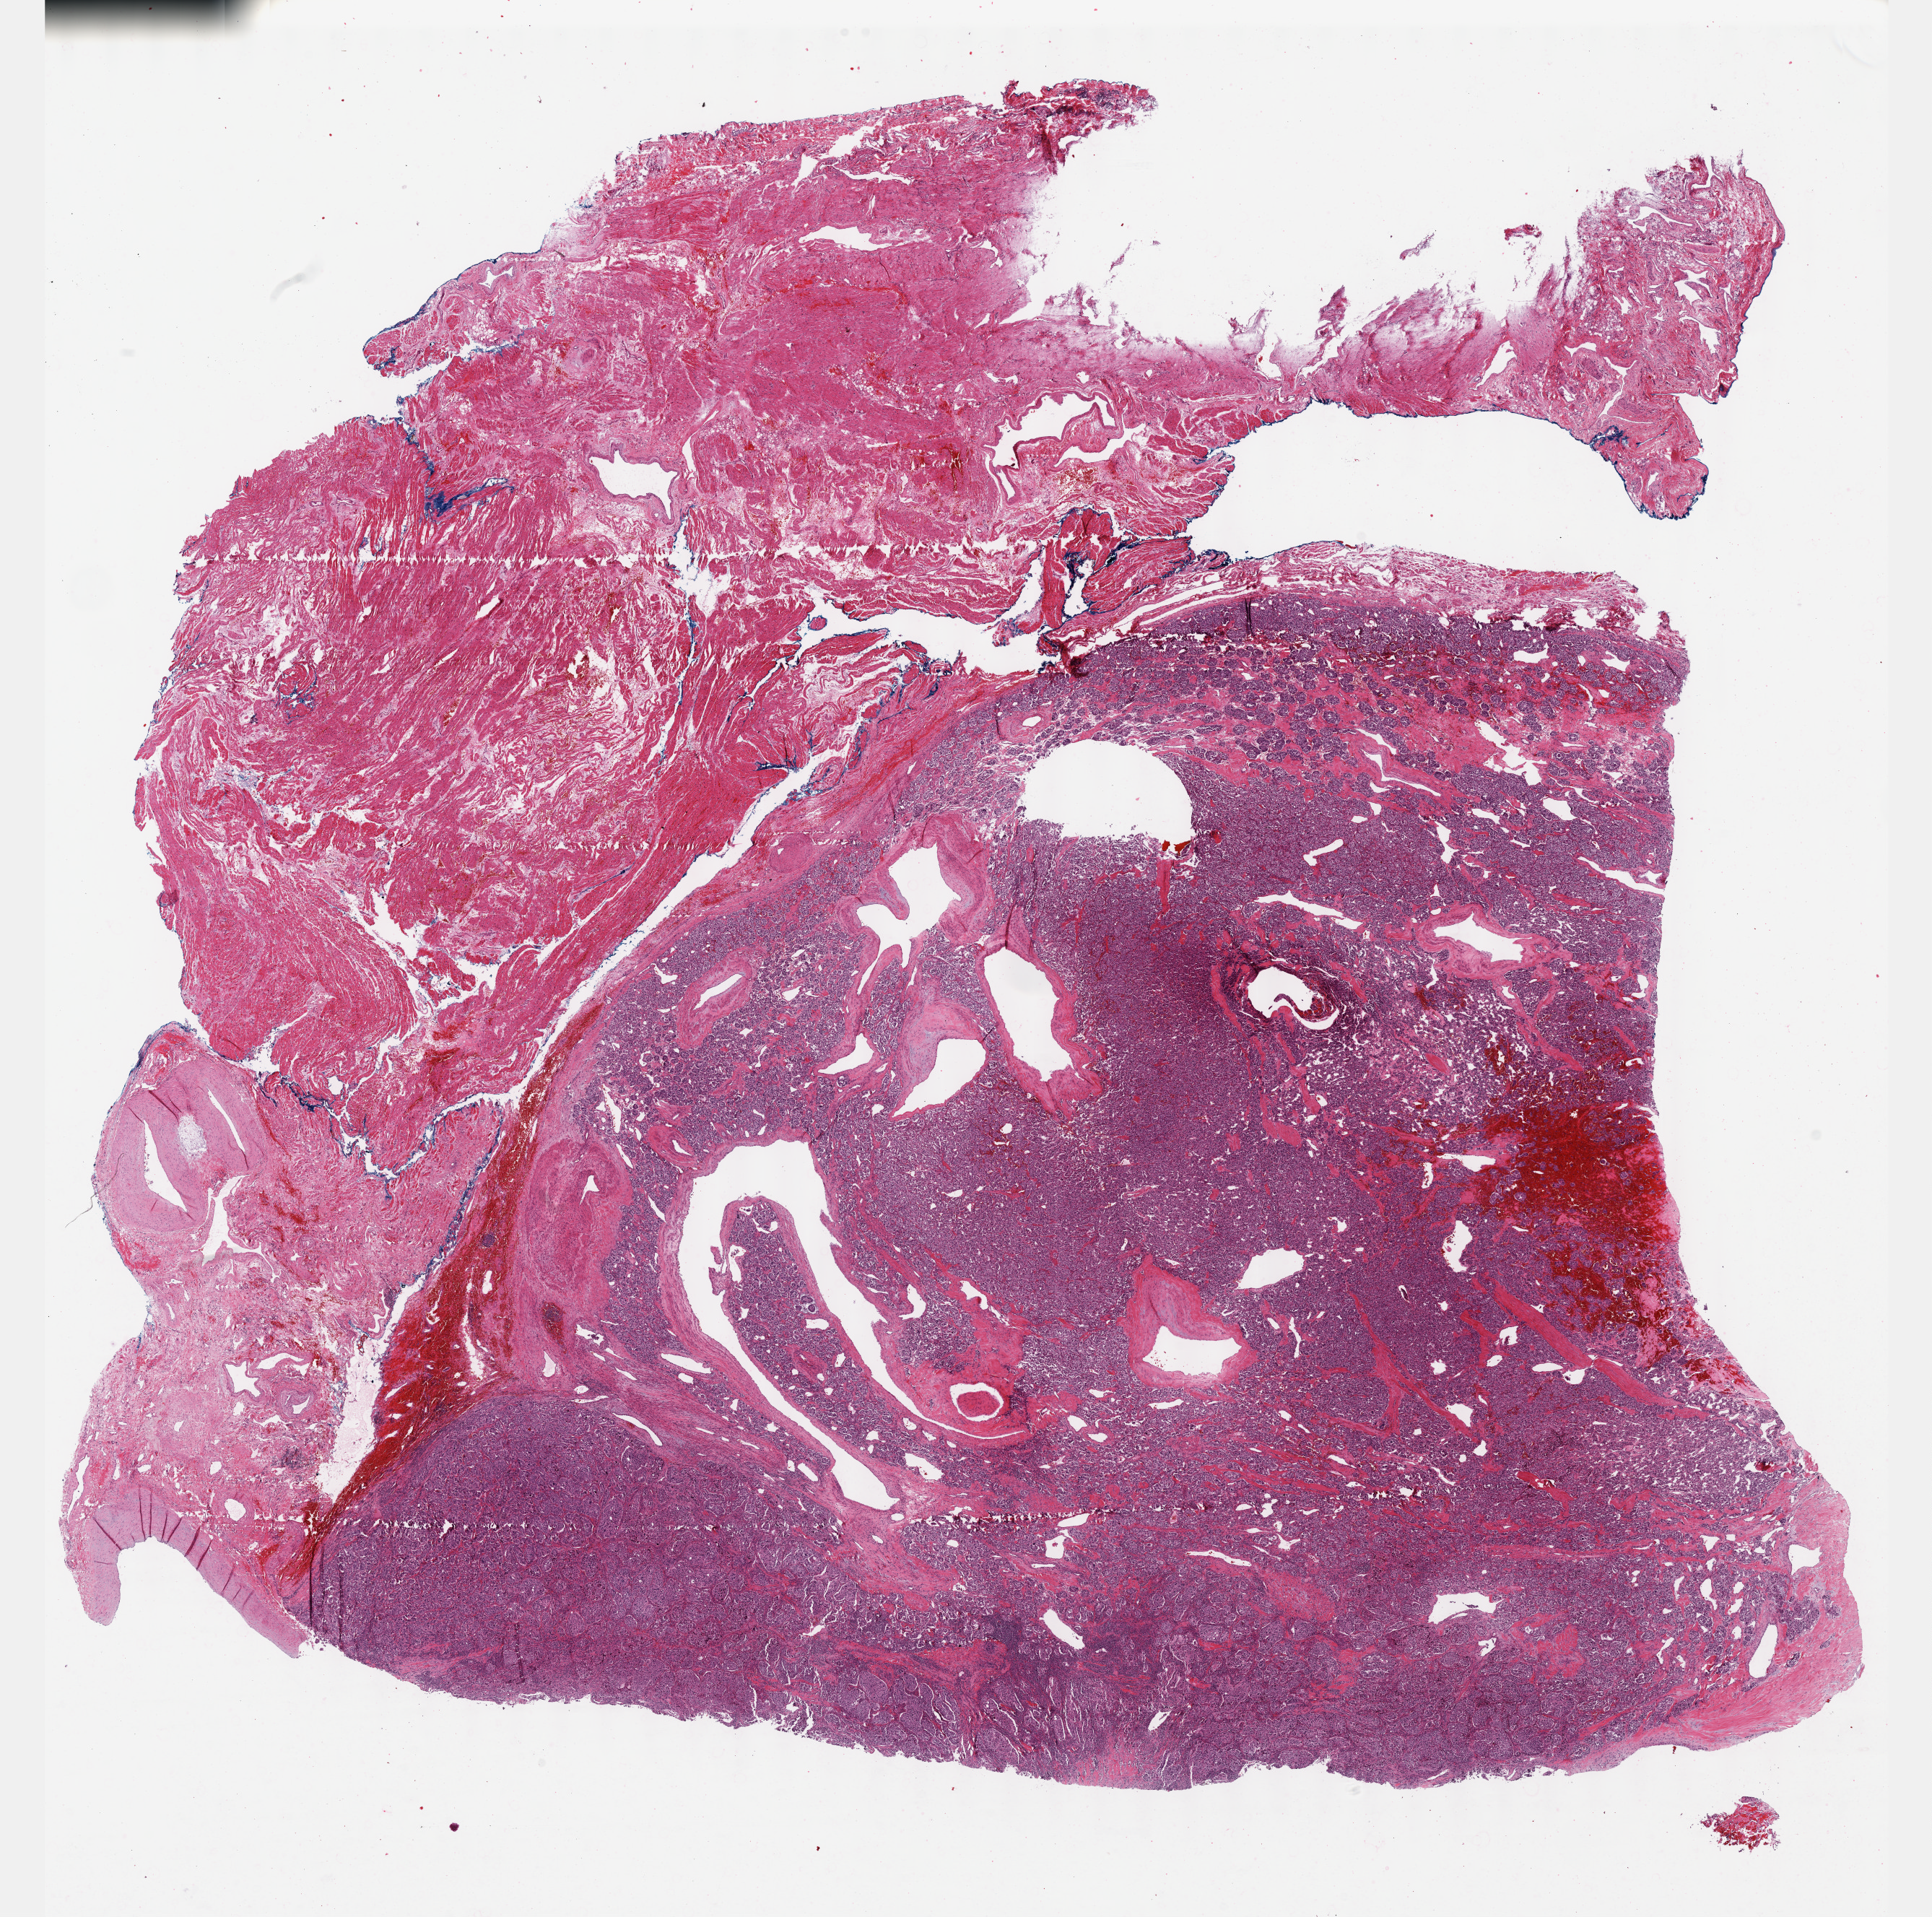
Digitized H&E-stained tissue section (whole slide) — low-resolution overview of the scanned area, about 21.6 x 21.5 mm, FFPE section, heart, mediastinum, and pleura, primary tumour sample. Patient: female, age at initial diagnosis 47 years.
* histologic diagnosis: Extra-adrenal paraganglioma, malignant (mediastinum, NOS)